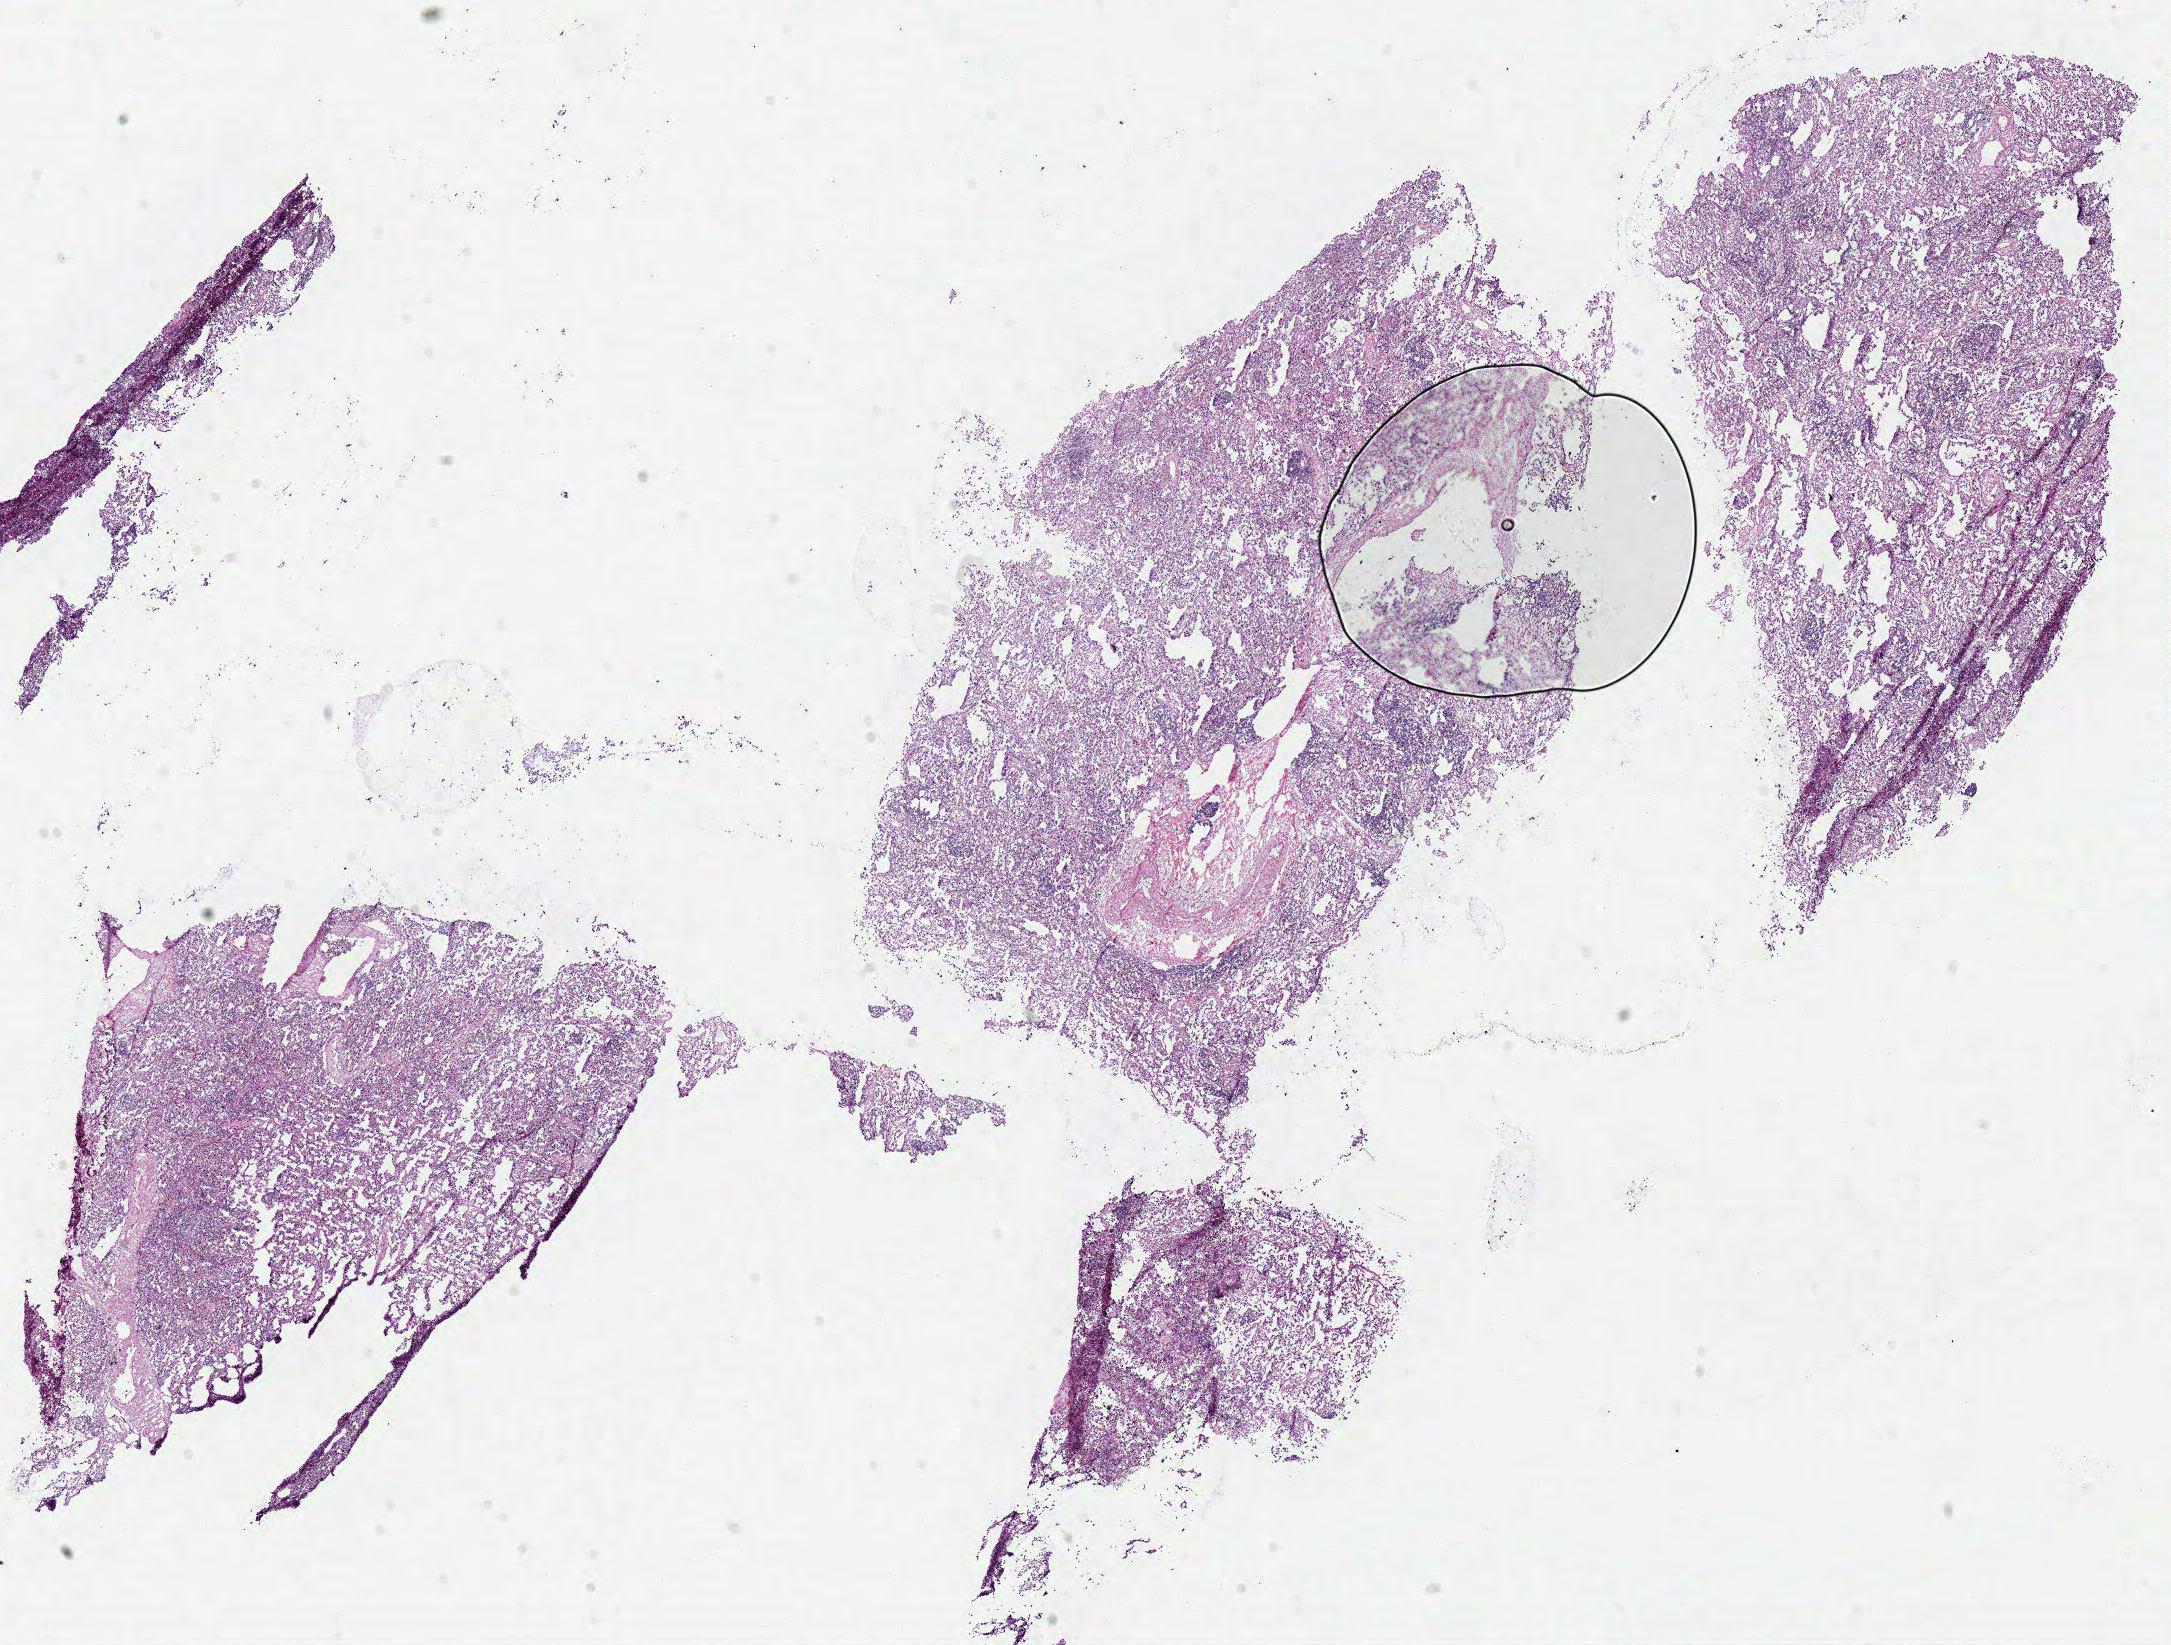
Digitized H&E tissue section (whole slide) — a low-resolution overview of the entire scanned area, about 17.1 x 13.0 mm. Frozen section from the top of the tissue portion. Sample: primary tumour, lung. Female patient; age at initial diagnosis 79 years. Composition of this section per pathologist review: tumour cells 85%, tumour nuclei 80%, normal cells 0%, stromal cells 15%, necrosis 0%.
* laterality: right
* diagnosis: Adenocarcinoma, NOS (lower lobe, lung)
* AJCC pathologic stage: IB (6th edition)